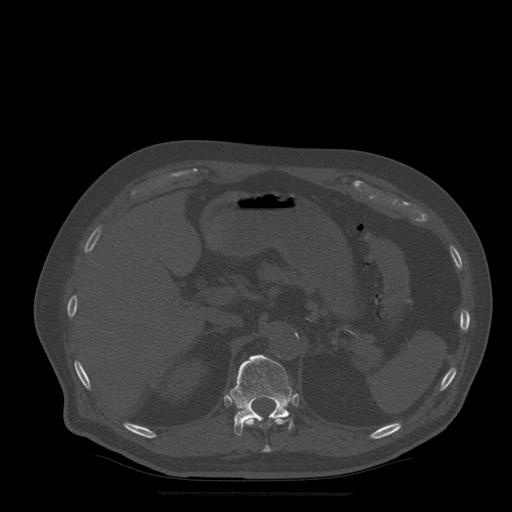
CT including the spine, one axial slice. Slice 228 of 522 in the series (ordered by position). Bone window (W 1800 / L 400 HU). 1.25 mm slice thickness. 512 × 512 image matrix. Patient age 72 years. Case-level facts recorded for this patient, not image findings: primary cancer: prostate.
Structures marked on this image (semi-automatically segmented with operator editing):
- T11 vertebra: bounding box (x1, y1, x2, y2) in pixels: (246, 415, 289, 453)
- T12 vertebra: (230, 355, 294, 436)